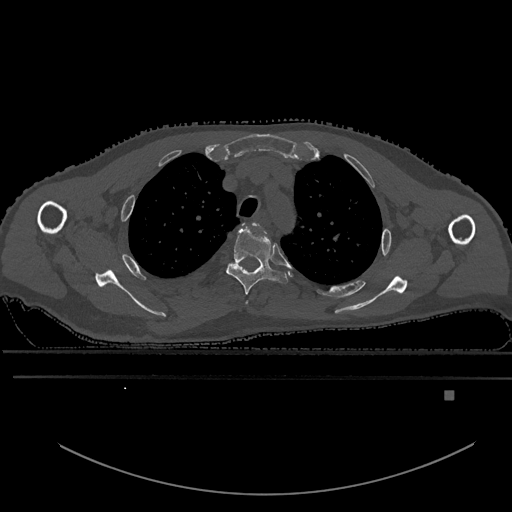
CT including the spine, one axial slice; bone window (W 1800 / L 400 HU); 0.5 mm slice thickness; 512 × 512 image matrix, field of view 456 × 456 mm. Patient: male, 82 years. From the clinical record (not read from this slice): primary cancer: prostate; vertebrae with lytic lesions (as recorded): T11, T9, T8, T2.
Annotated regions visible in this slice (semi-automatically segmented with operator editing):
- T2 vertebra: box from (x=242, y=222) to (x=261, y=303) px
- T3 vertebra: (x=226, y=222)–(x=289, y=295)